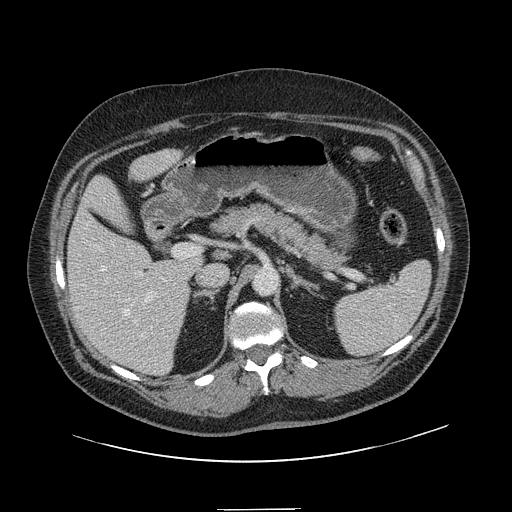
Contrast-enhanced abdominal CT, one axial slice. Slice 80 of 154 in the series (ordered by position). Intravenous contrast given. Soft-tissue window (W 400 / L 40 HU). 2.5 mm slice thickness. 512 × 512 image matrix, field of view 451 × 451 mm. Male patient, age 61 years. From the clinical record (not read from this slice): diagnosis: colorectal cancer liver metastases, imaged before liver resection; multiple liver metastases: yes; largest metastasis: 2.6 cm; chemotherapy before resection: no.
Outlined on this slice (outlined manually by an expert reader):
- hepatic veins: bounding box (x1, y1, x2, y2) in pixels: (101, 266, 153, 337)
- liver: (68, 151, 202, 375)
- planned liver remnant (the part of the liver to remain after resection): (69, 151, 202, 365)
- portal vein (with intrahepatic branches): (95, 250, 200, 323)